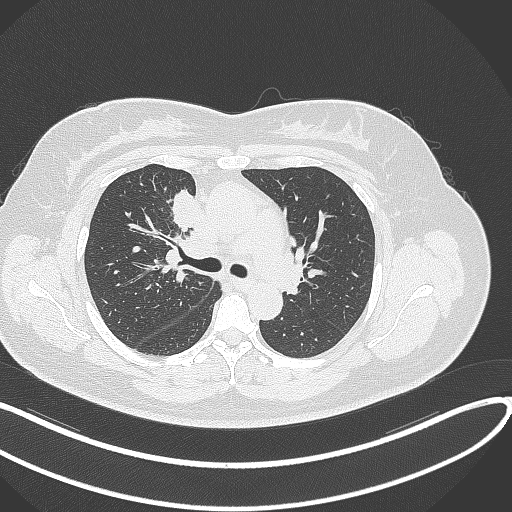
Chest CT, one axial slice; slice 179 of 303 in the series (ordered by position); reconstruction kernel B70f; 120 kVp; lung window (W 1500 / L -600 HU); 512 × 512 image matrix, field of view 400 × 400 mm. Patient: female, 46 years. From the clinical record (not read from this slice): clinical TNM (as recorded): T2a N1 M0.
Annotated regions visible in this slice (rectangle marked by the reading radiologist):
- lung tumour (recorded histology: adenocarcinoma): bounding box (x1, y1, x2, y2) in pixels: (165, 186, 207, 237)